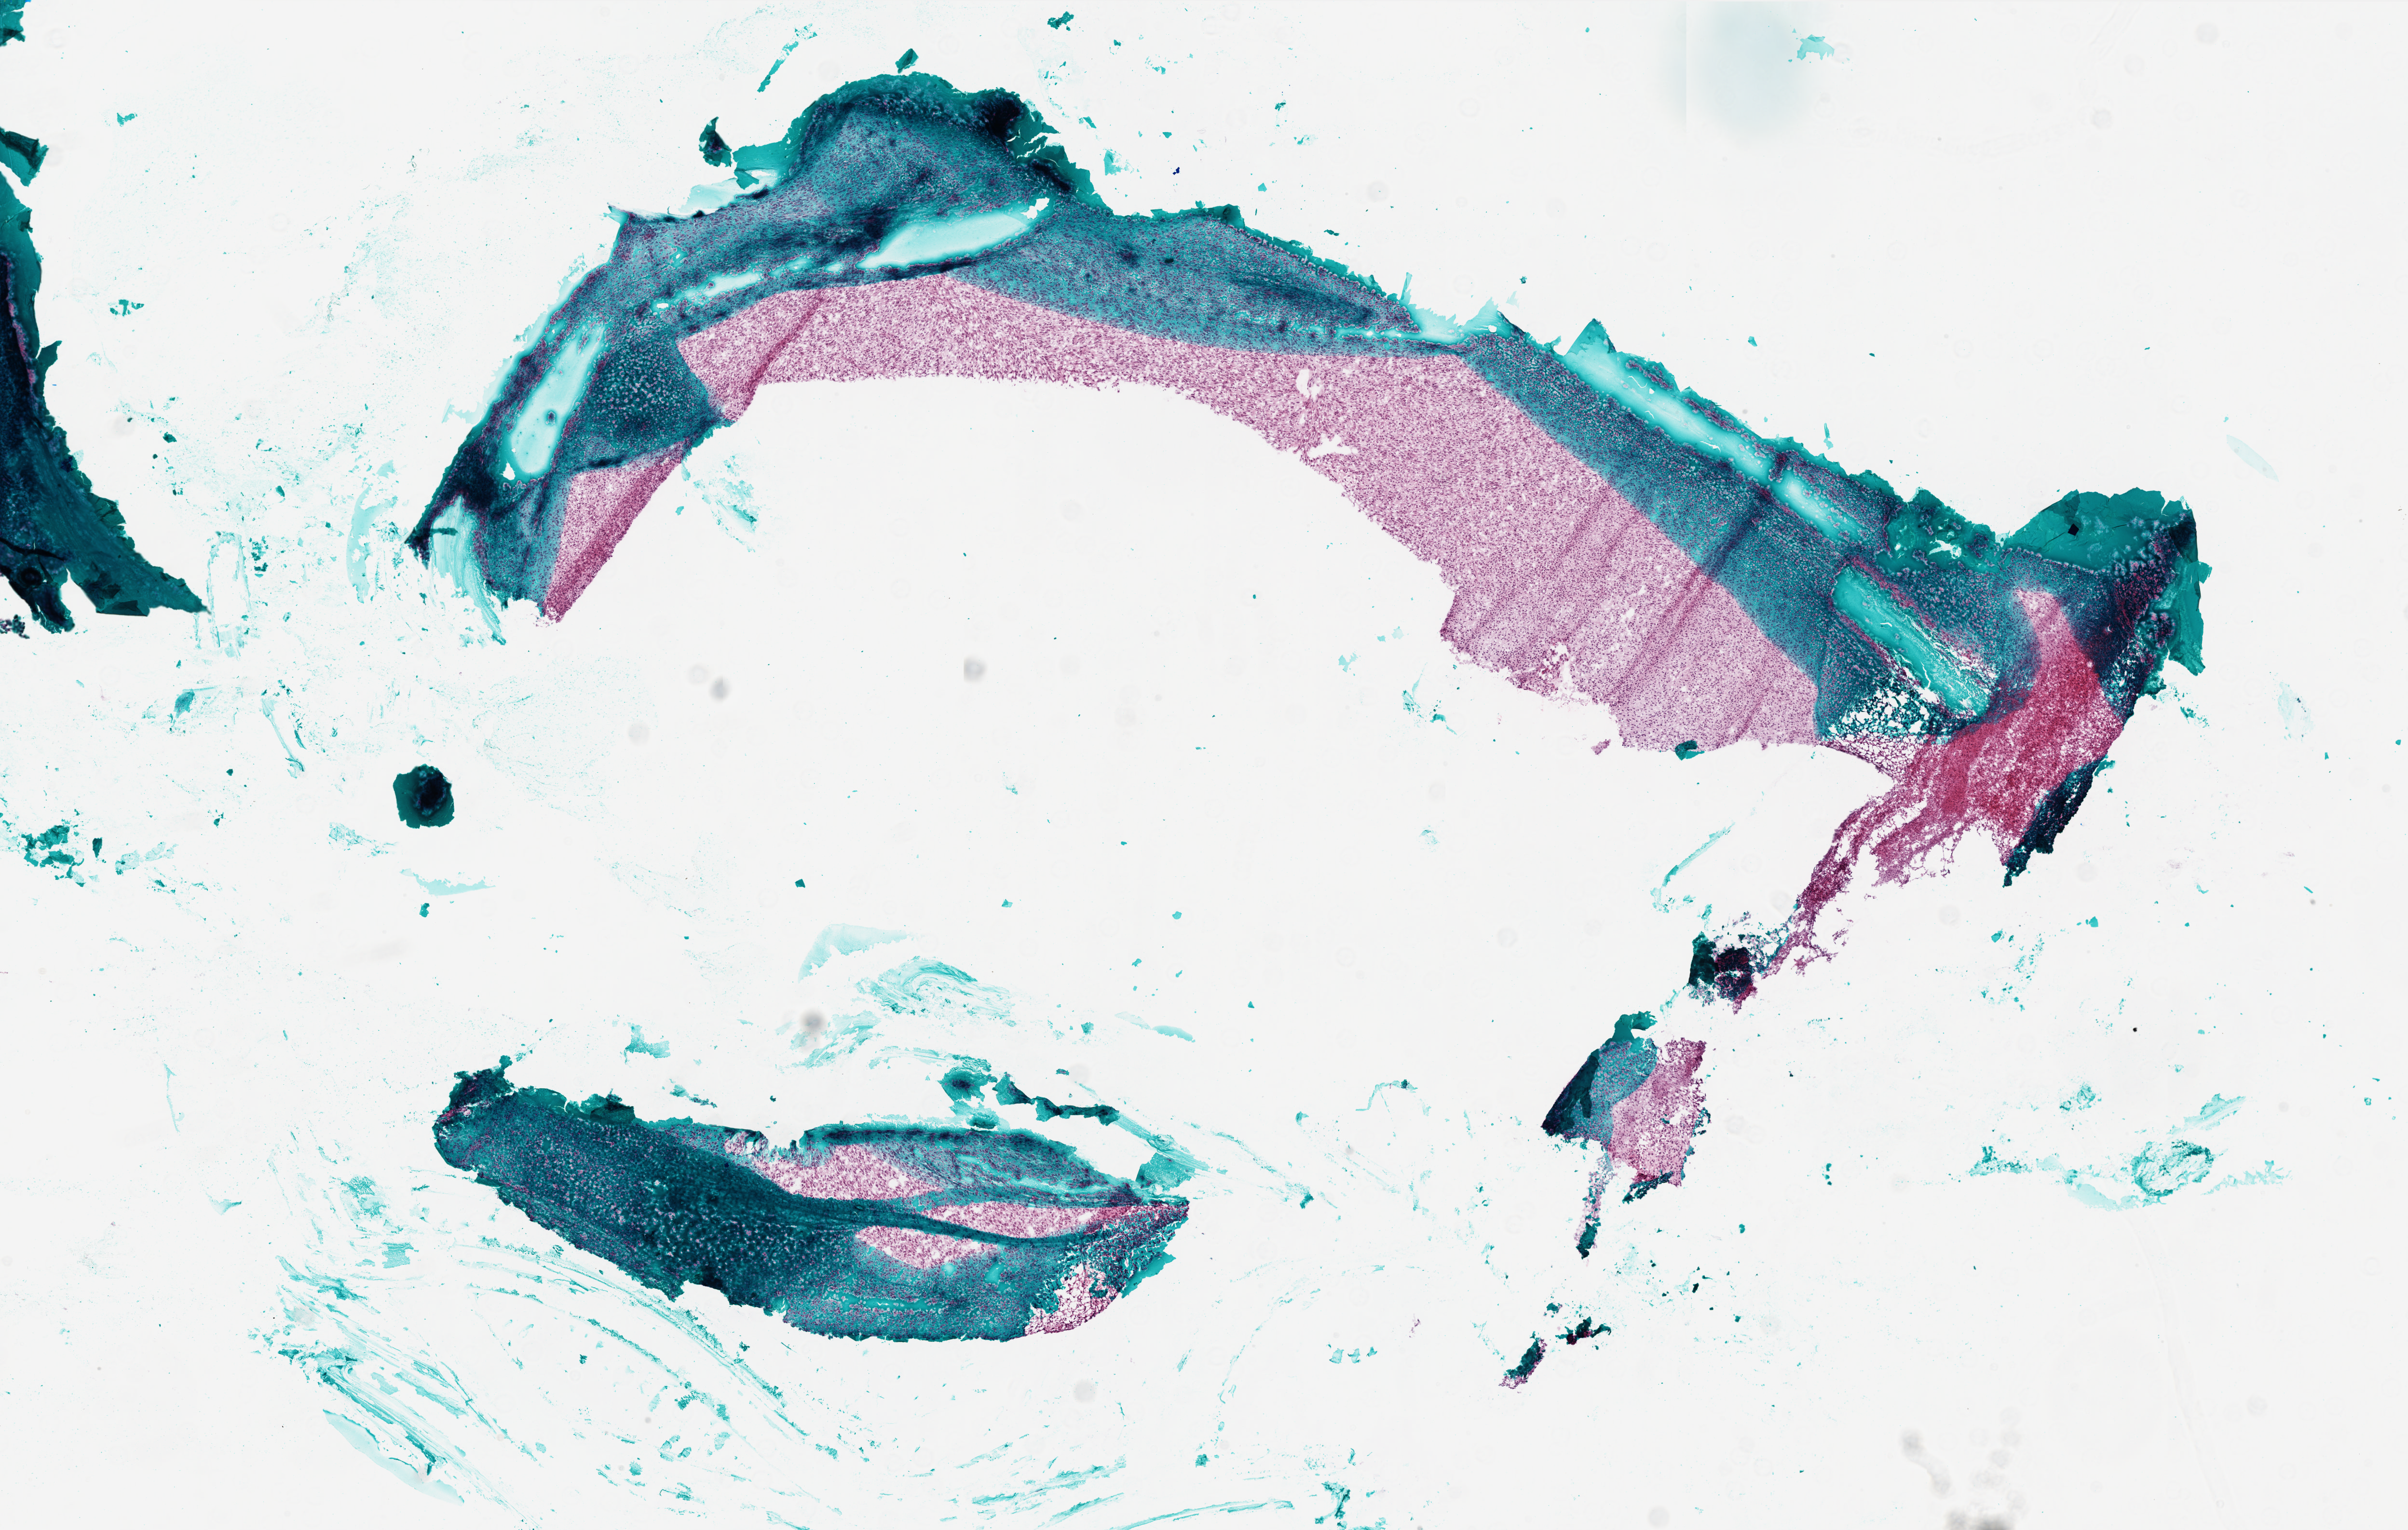
Hematoxylin and eosin (H&E) stained whole-slide image, low-resolution overview of the scanned area, about 10.0 x 6.3 mm (acquisition: 20x scan); frozen section from the bottom of the tissue portion; sample: primary tumour, brain. Female patient; age at initial diagnosis 61 years. Slide review estimates, as recorded: tumour cells 100%, tumour nuclei 100%, normal cells 0%, stromal cells 0%, necrosis 5%.
Pathologic diagnosis: Glioblastoma.